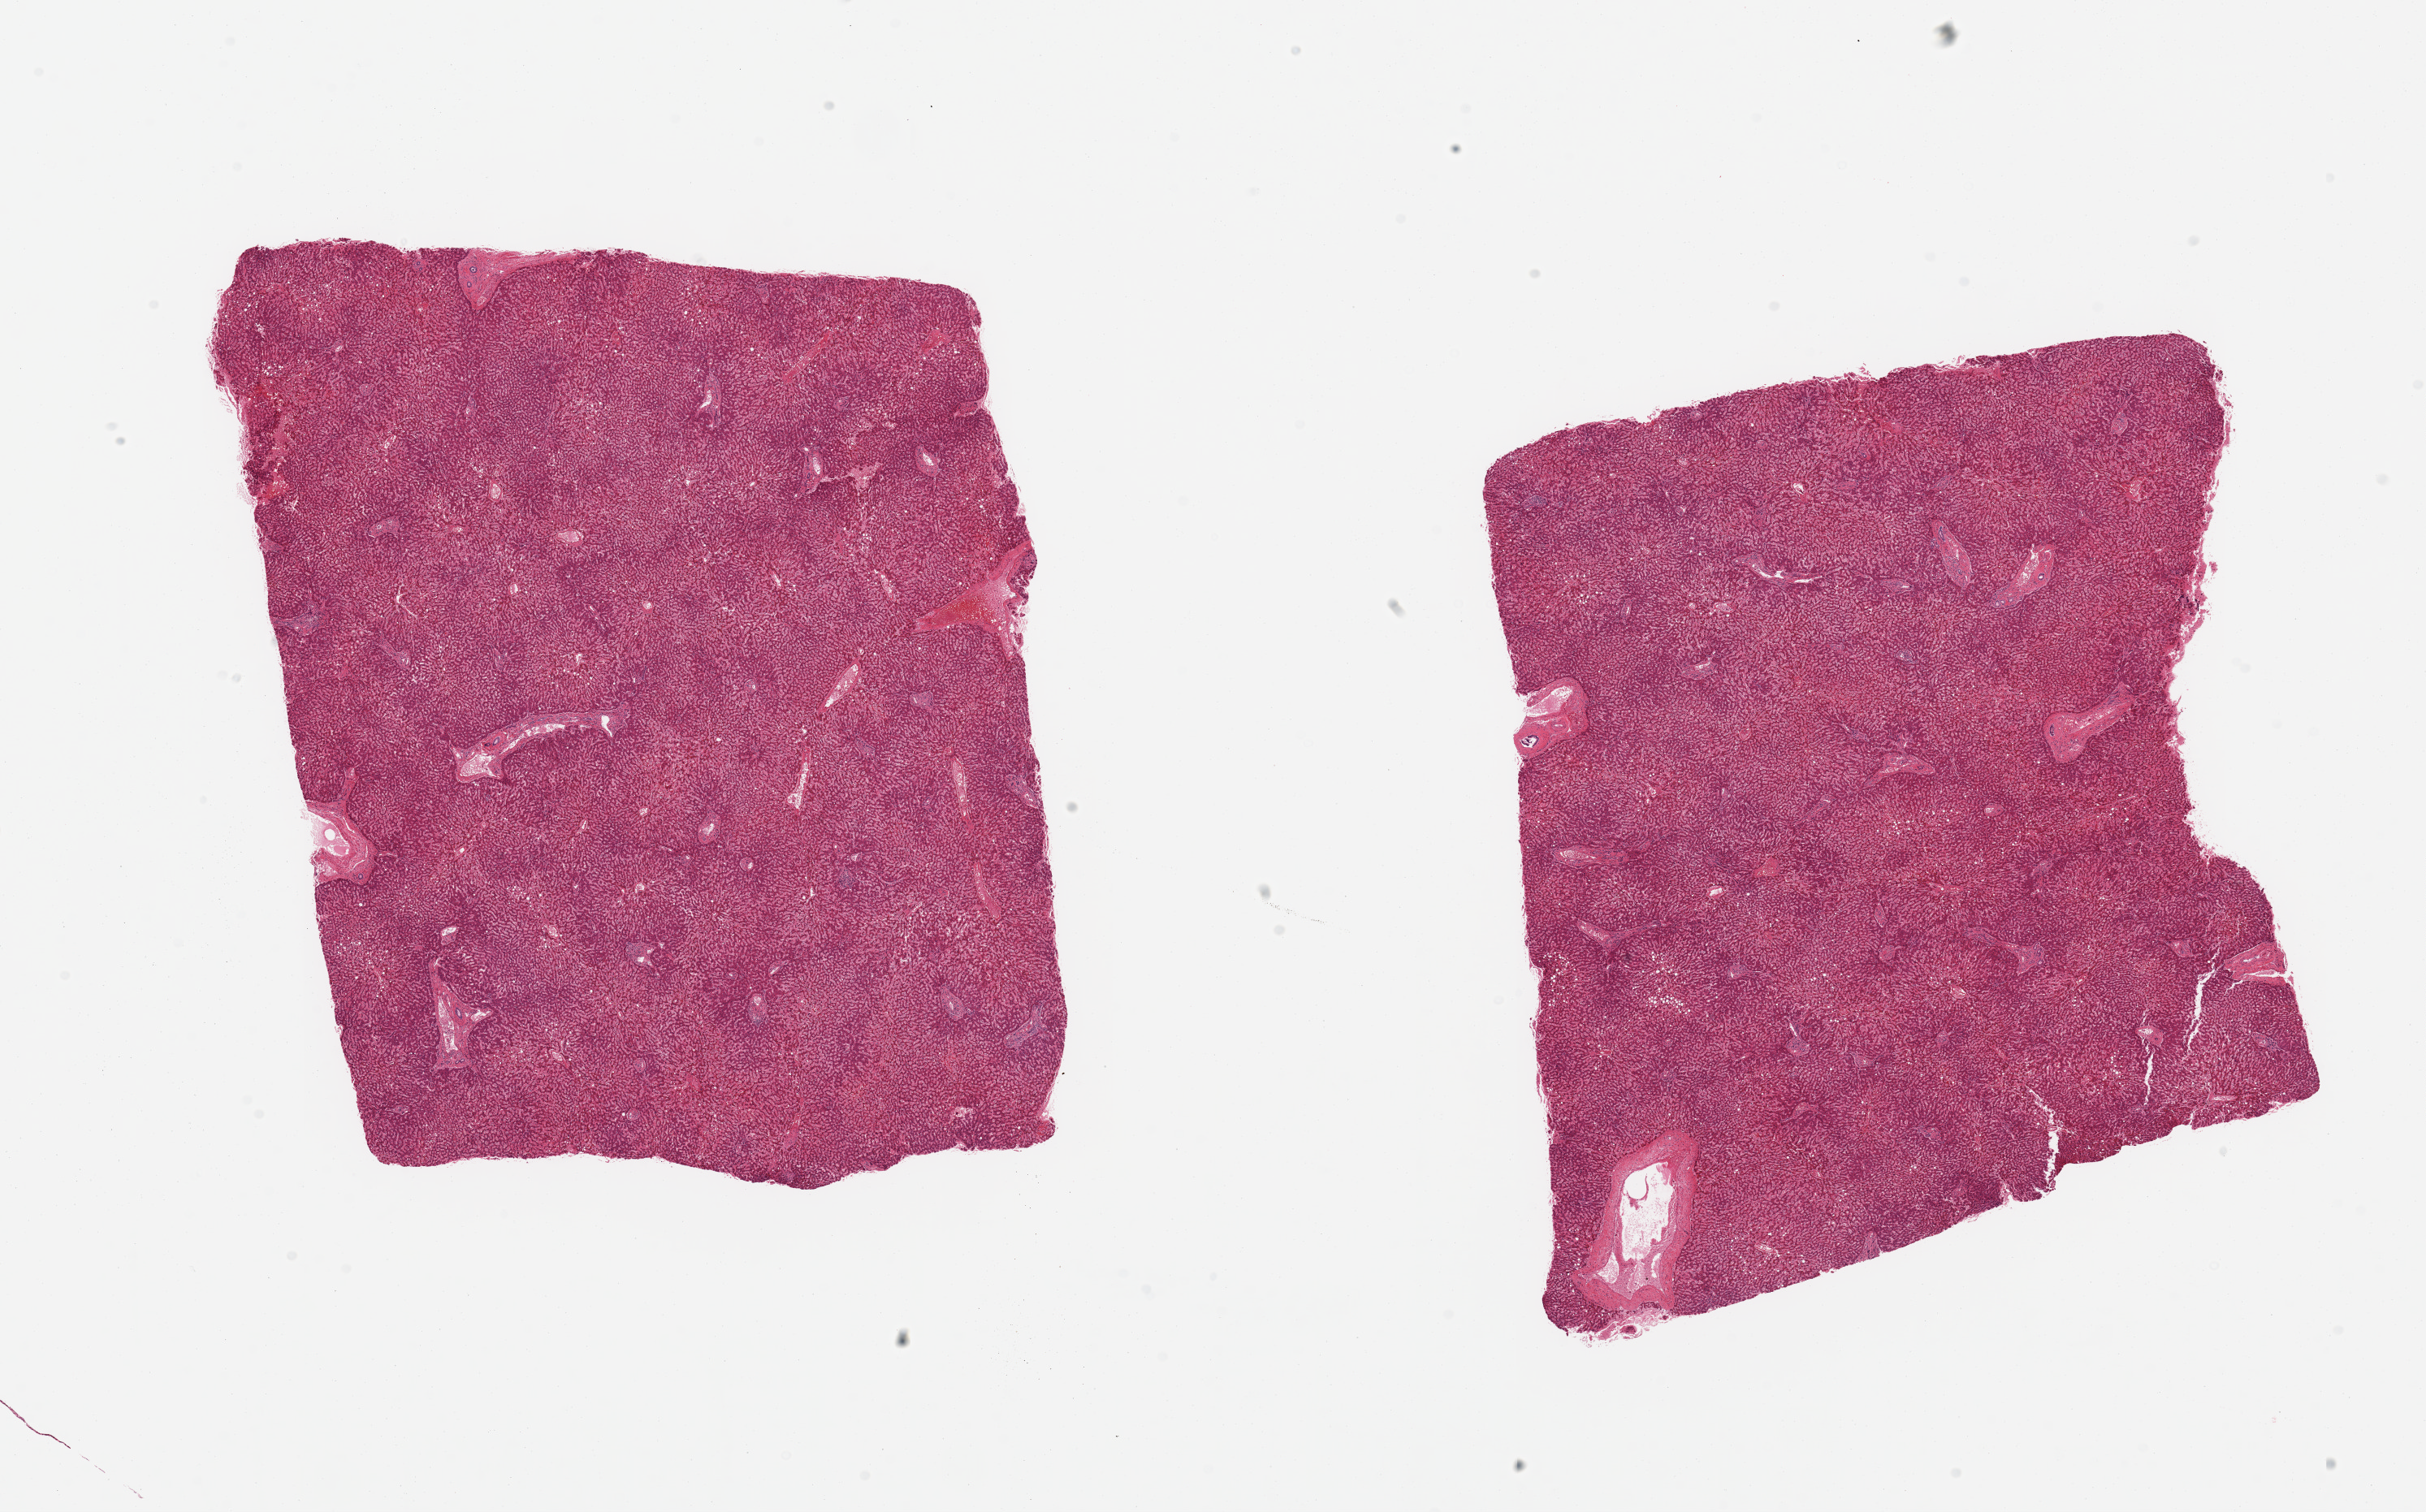
H&E whole-slide image, brightfield — shown as a low-resolution overview of the whole scanned area (about 23.6 x 14.7 mm, acquisition: 20x scan). PAXgene-fixed, paraffin-embedded tissue. Sampled site (target tissue): liver. Donor tissue sample. Male donor.
* pathologist's review note for this sample: 2 pieces mild-moderate passive congestion